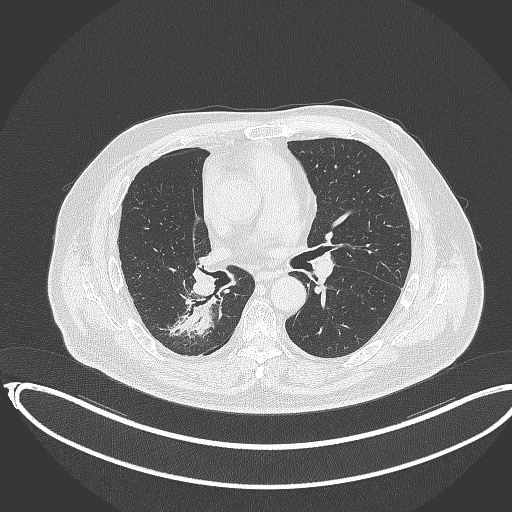
Chest CT, one axial slice; 120 kVp; lung window (W 1500 / L -600 HU); 1 mm slice thickness; 512 × 512 image matrix. Patient: male, 68 years. Case-level facts recorded for this patient, not image findings: clinical TNM (as recorded): T2a N0 M0.
Outlined on this slice (bounding box drawn by a radiologist):
- lung tumour (recorded histology: adenocarcinoma): bounding box (x1, y1, x2, y2) in pixels: (166, 293, 222, 335)